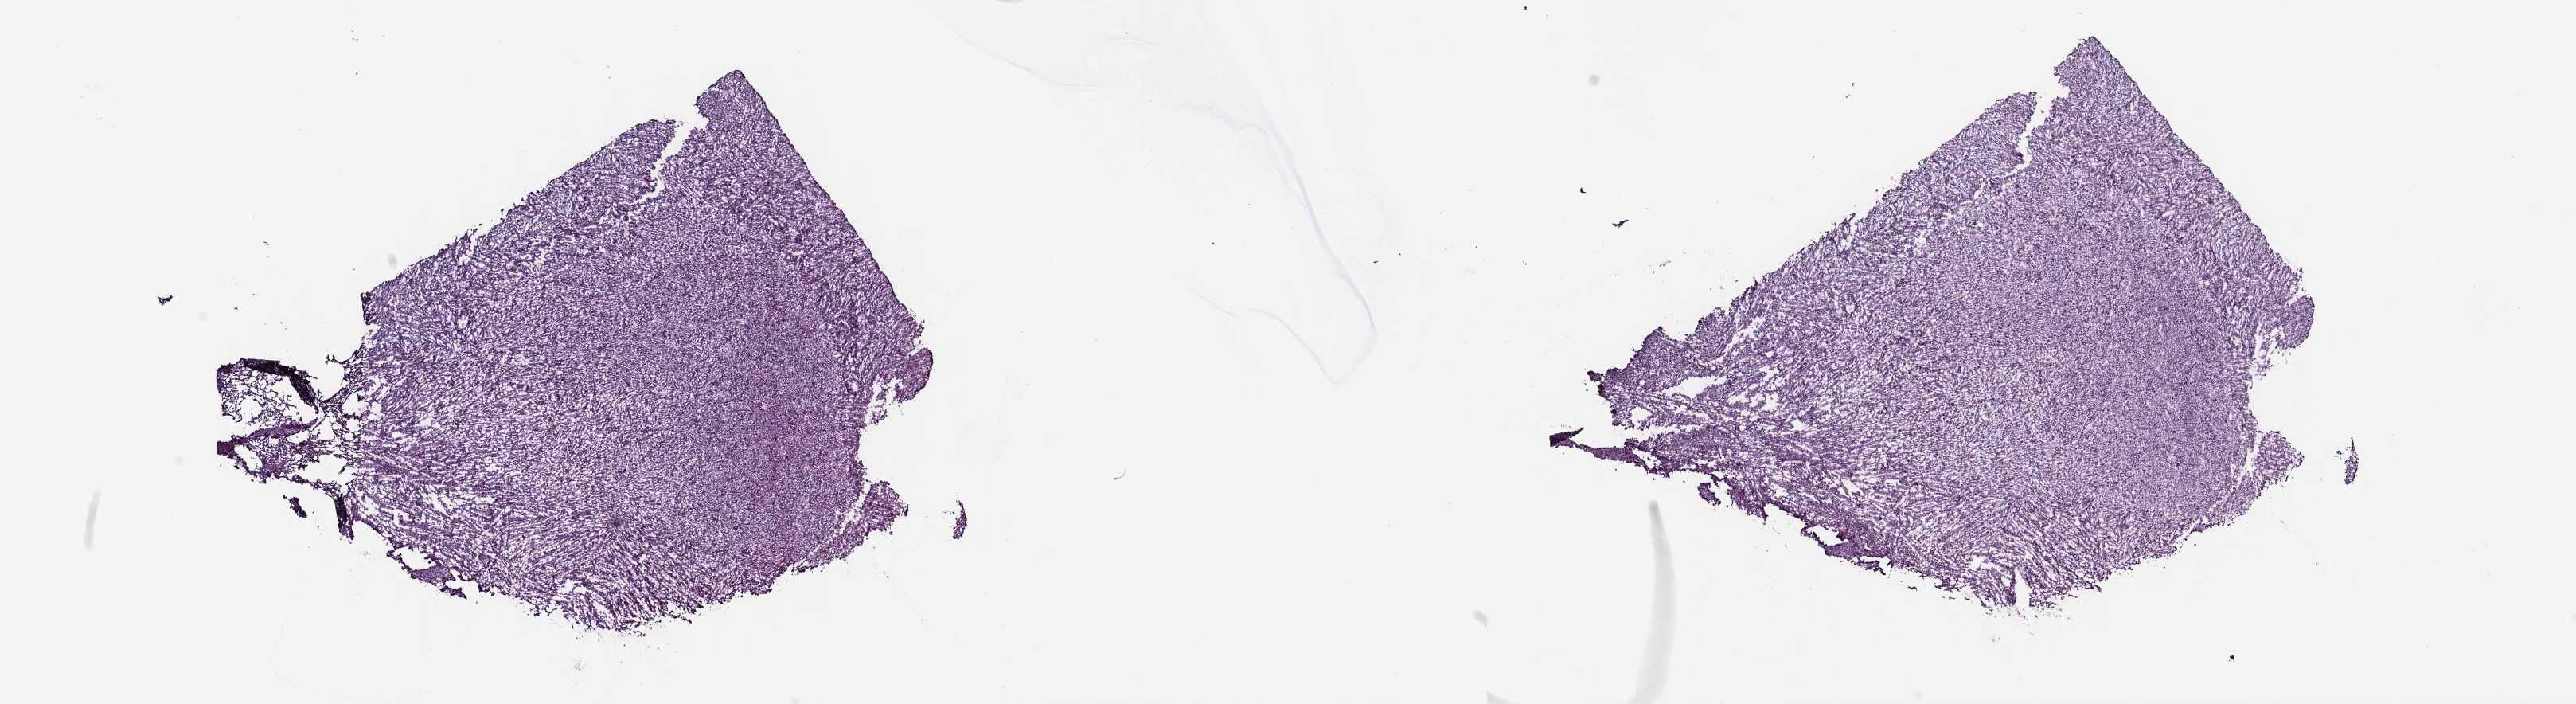
Digitized Hematoxylin and eosin (H&E) stained tissue section (whole slide) — a low-resolution overview of the entire scanned area, about 26.2 x 7.2 mm, frozen section from the top of the tissue portion, sample: primary tumour, connective, subcutaneous and other soft tissues. Female, age 78 years at initial diagnosis. Pathologist review of this section (percent, as recorded): tumour cells 100%, tumour nuclei 80%, normal cells 0%, stromal cells 0%, necrosis 0%. Inflammatory infiltration, as recorded: lymphocyte infiltration 2%, monocyte infiltration 0%, neutrophil infiltration 0%.
- diagnosis: Undifferentiated sarcoma